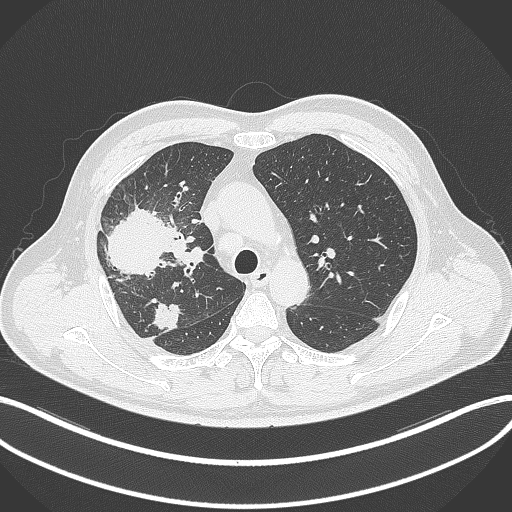
Chest CT, one axial slice; slice 233 of 348 in the series (ordered by position); reconstruction kernel B70f; lung window (W 1500 / L -600 HU); 1 mm slice thickness; 512 × 512 image matrix, field of view 400 × 400 mm. Male patient, age 55 years. From the clinical record (not read from this slice): clinical TNM (as recorded): T3 N2 M1.
Annotated regions visible in this slice (bounding box drawn by a radiologist):
- lung tumour (recorded histology: adenocarcinoma): box from (x=103, y=205) to (x=173, y=279) px